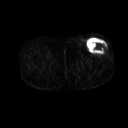
FDG PET of an extremity soft-tissue mass (from a PET/CT study), one axial slice; slice 237 of 267 in the series (ordered by position); 3.27 mm slice thickness; 128 × 128 image matrix, field of view 500 × 500 mm. Patient: male, 64 years. Case-level facts recorded for this patient, not image findings: histological type: extraskeletal osteosarcoma; grade: high; site of the primary tumour: thigh.
Outlined on this slice (expert contour drawn on MRI and transferred to this co-registered scan by the dataset authors):
- gross tumour volume (mass): bounding box [x1, y1, x2, y2] px = [87, 39, 108, 53]